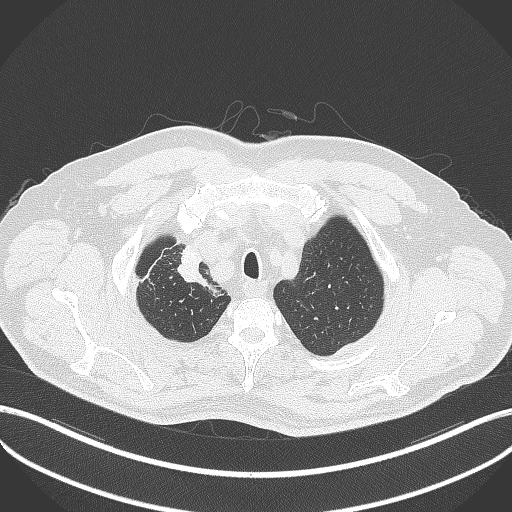
Chest CT, one axial slice. Slice 335 of 411 in the series (ordered by position). Reconstruction kernel B70f. 120 kVp. Lung window (W 1500 / L -600 HU). 512 × 512 image matrix, field of view 400 × 400 mm. Patient: male, 60 years. From the clinical record (not read from this slice): clinical TNM (as recorded): T1b N1 M0.
Structures marked on this image (rectangle marked by the reading radiologist):
- lung tumour (recorded histology: squamous cell carcinoma): bounding box (x1, y1, x2, y2) in pixels: (176, 244, 210, 287)